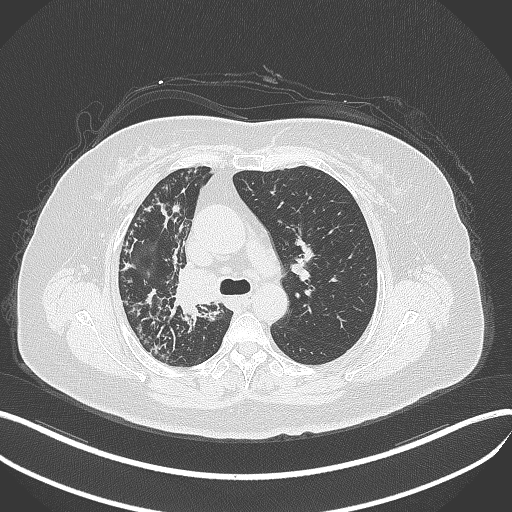
Chest CT, one axial slice; slice 240 of 376 in the series (ordered by position); 120 kVp; lung window (W 1500 / L -600 HU); 512 × 512 image matrix, field of view 400 × 400 mm. Female patient, age 60 years. Case-level facts recorded for this patient, not image findings: clinical TNM (as recorded): T1c N0 M0; histopathological grade: G1-G2.
Annotated regions visible in this slice (rectangle marked by the reading radiologist):
- lung tumour (recorded histology: squamous cell carcinoma): bounding box [x1, y1, x2, y2] px = [169, 264, 224, 312]